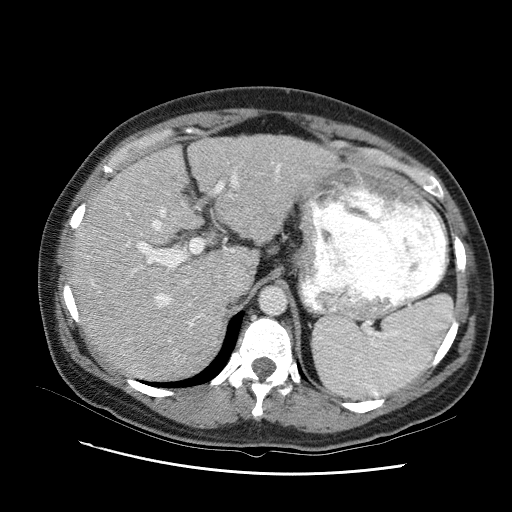
Contrast-enhanced abdominal CT (liver protocol), one axial slice; slice 66 of 95 in the series (ordered by position); reconstruction kernel STANDARD; 120 kVp; one of 2 acquisitions stored at this slice position; soft-tissue window (W 400 / L 40 HU); 2.5 mm slice thickness; 512 × 512 image matrix, field of view 360 × 360 mm. Case-level facts recorded for this patient, not image findings: diagnosis: hepatocellular carcinoma (patient treated with transarterial chemoembolisation; whether this scan precedes or follows treatment is not stated here); TNM stage (as recorded): Stage-I; Child-Pugh class: B; tumour differentiation: moderately differentiated; tumour nodularity: uninodular.
Structures marked on this image (semi-automatic segmentation, software-assisted and operator-edited):
- abdominal aorta: bounding box (x1, y1, x2, y2) in pixels: (259, 287, 285, 314)
- liver parenchyma outside the tumour (the mass and vessels are separate outlines, so this box may not span the whole liver): (68, 132, 341, 368)
- liver vessels: (111, 150, 307, 324)